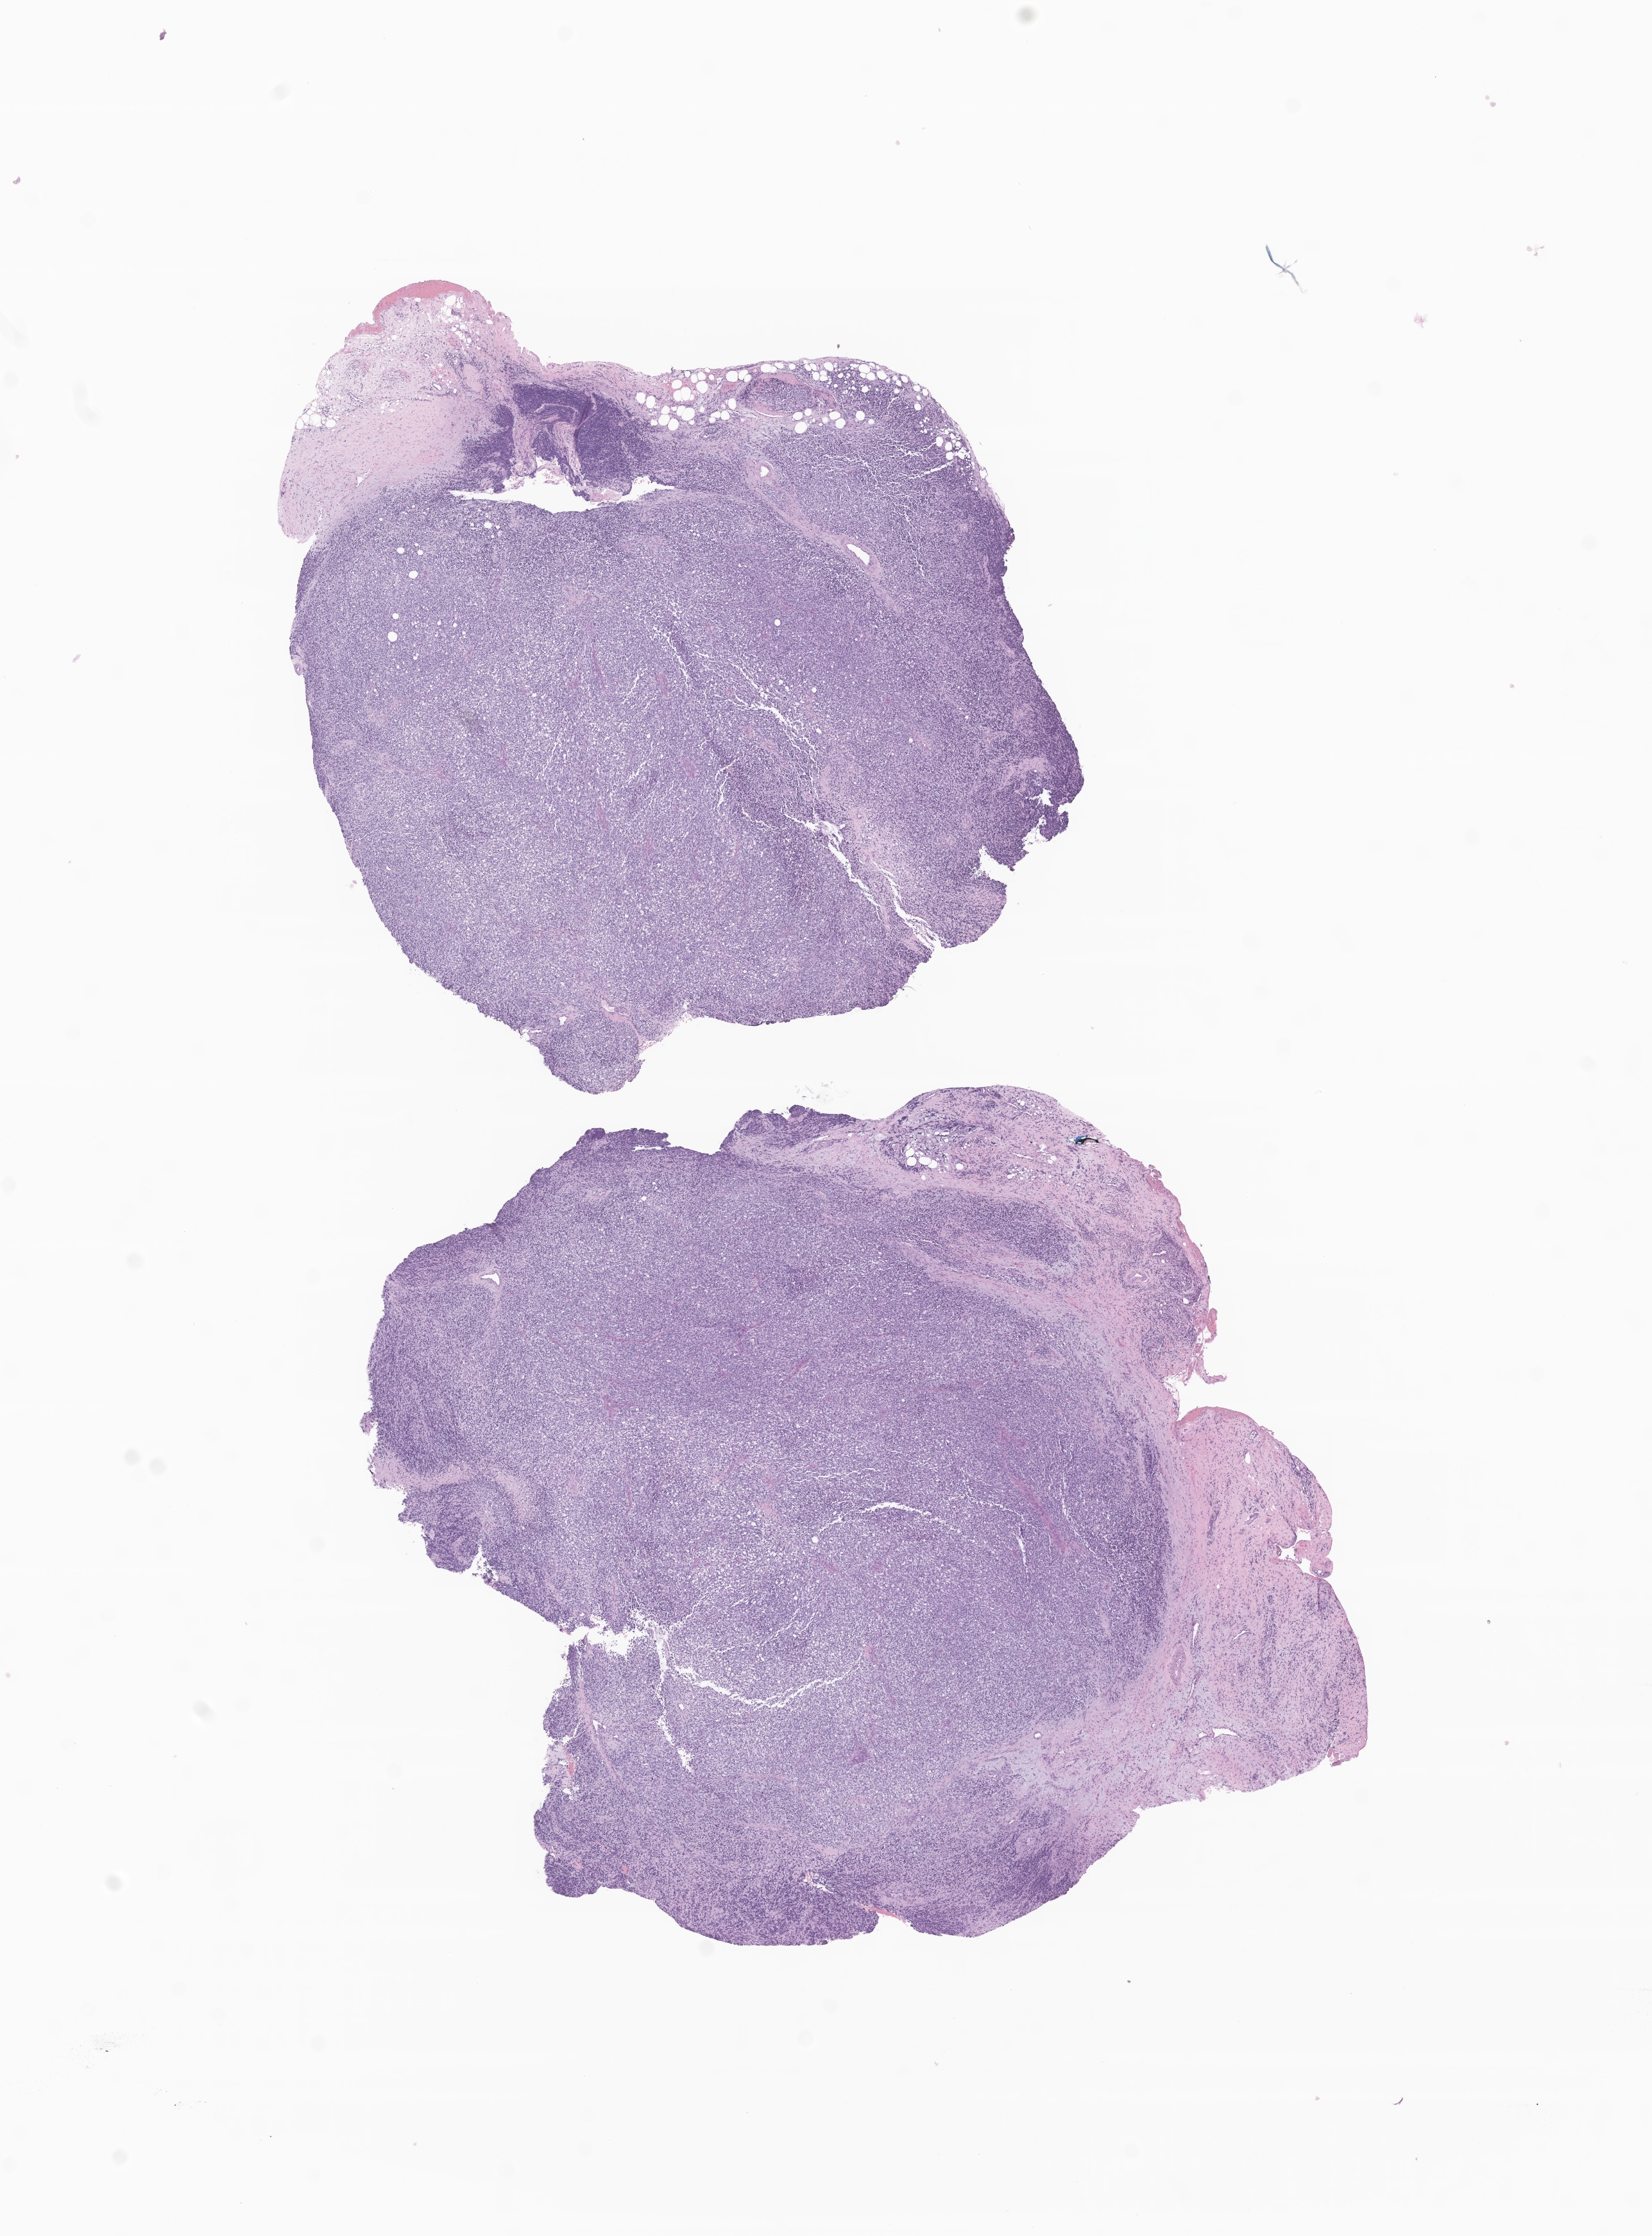
Digitized H&E-stained section of tumor tissue from the orbit — low-resolution overview of the scanned area, about 10.9 x 14.7 mm; formalin-fixed paraffin-embedded section. Female patient, age 177 months (14 years 9 months).
* recorded diagnosis: Embryonal rhabdomyosarcoma, NOS